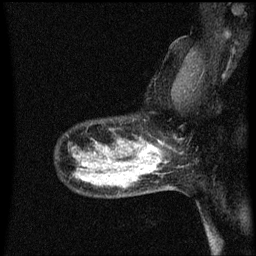
Breast MRI (dynamic contrast-enhanced), one sagittal slice; position 48 of 60 along the scan axis; dynamic contrast-enhanced series, image 2 of 3 at this slice position (ordered by acquisition); 1.5 T; TE 4.2 ms, TR 8.4 ms; 2 mm slice thickness; 256 × 256 image matrix, field of view 200 × 200 mm. Patient: female, 50 years.
Outlined on this slice (semi-automatic segmentation, software-assisted and operator-edited):
- analysis volume of interest (the breast-tissue region the enhancement analysis was run in; not a lesion): box from (x=100, y=140) to (x=153, y=171) px
- tumour enhancement mask (voxels above the 70 % enhancement threshold inside the analysis volume of interest): (x=116, y=142)–(x=153, y=171)